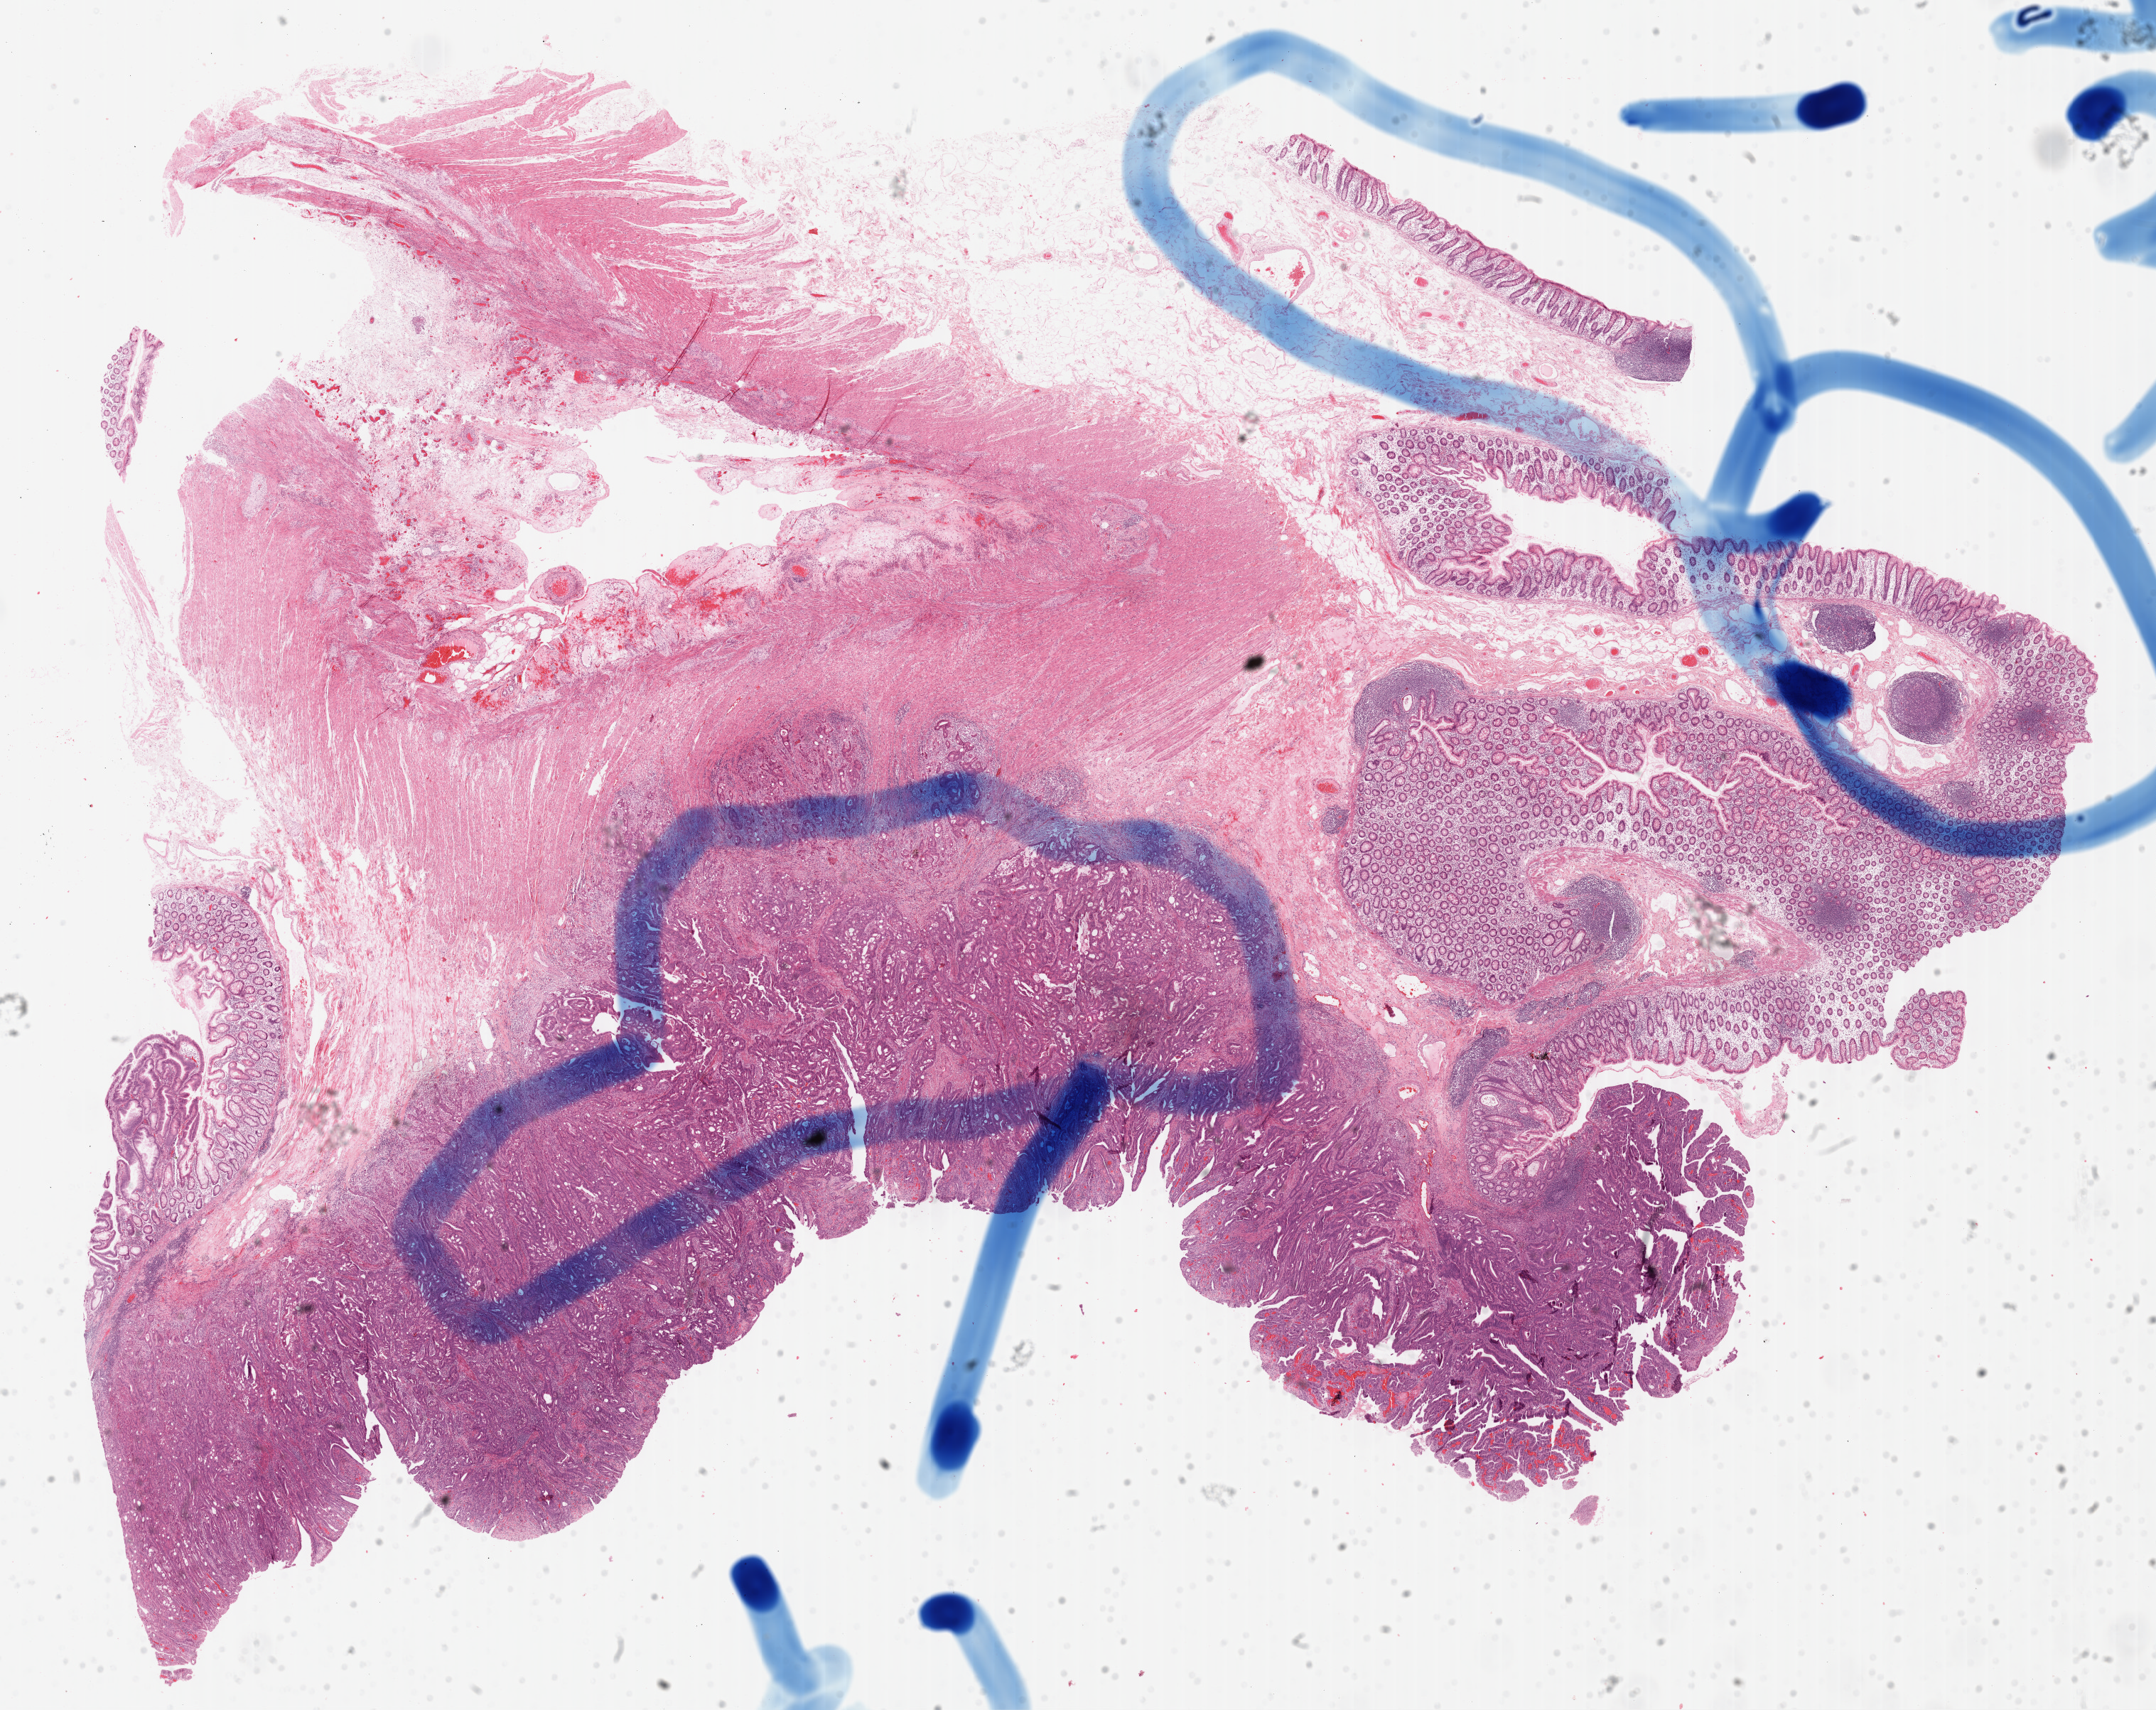
Digitized H&E-stained tissue section (whole slide) — a low-resolution overview of the entire scanned area, about 24.0 x 19.0 mm (slide scanned at 40x), formalin-fixed paraffin-embedded (FFPE) diagnostic section, primary tumour sample from the colon. Patient: female, age at initial diagnosis 67 years.
Pathologic diagnosis: Adenocarcinoma, NOS (cecum).